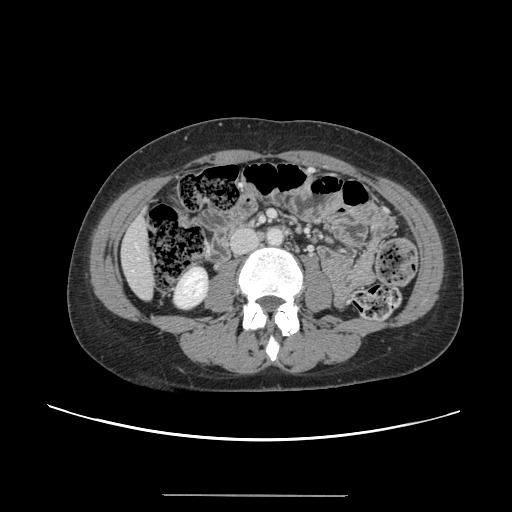
Contrast-enhanced abdominal CT, one axial slice. Position 26 of 144 along the scan axis. 120 kVp. Soft-tissue window (W 400 / L 40 HU). 2.5 mm slice thickness. 512 × 512 image matrix, field of view 380 × 380 mm. Female patient, age 53 years. From the clinical record (not read from this slice): diagnosis: colorectal cancer liver metastases, imaged before liver resection; multiple liver metastases: yes.
Structures marked on this image (manually delineated by an expert):
- liver: box from (x=123, y=214) to (x=154, y=299) px
- planned liver remnant (the part of the liver to remain after resection): (x=122, y=213)–(x=154, y=299)